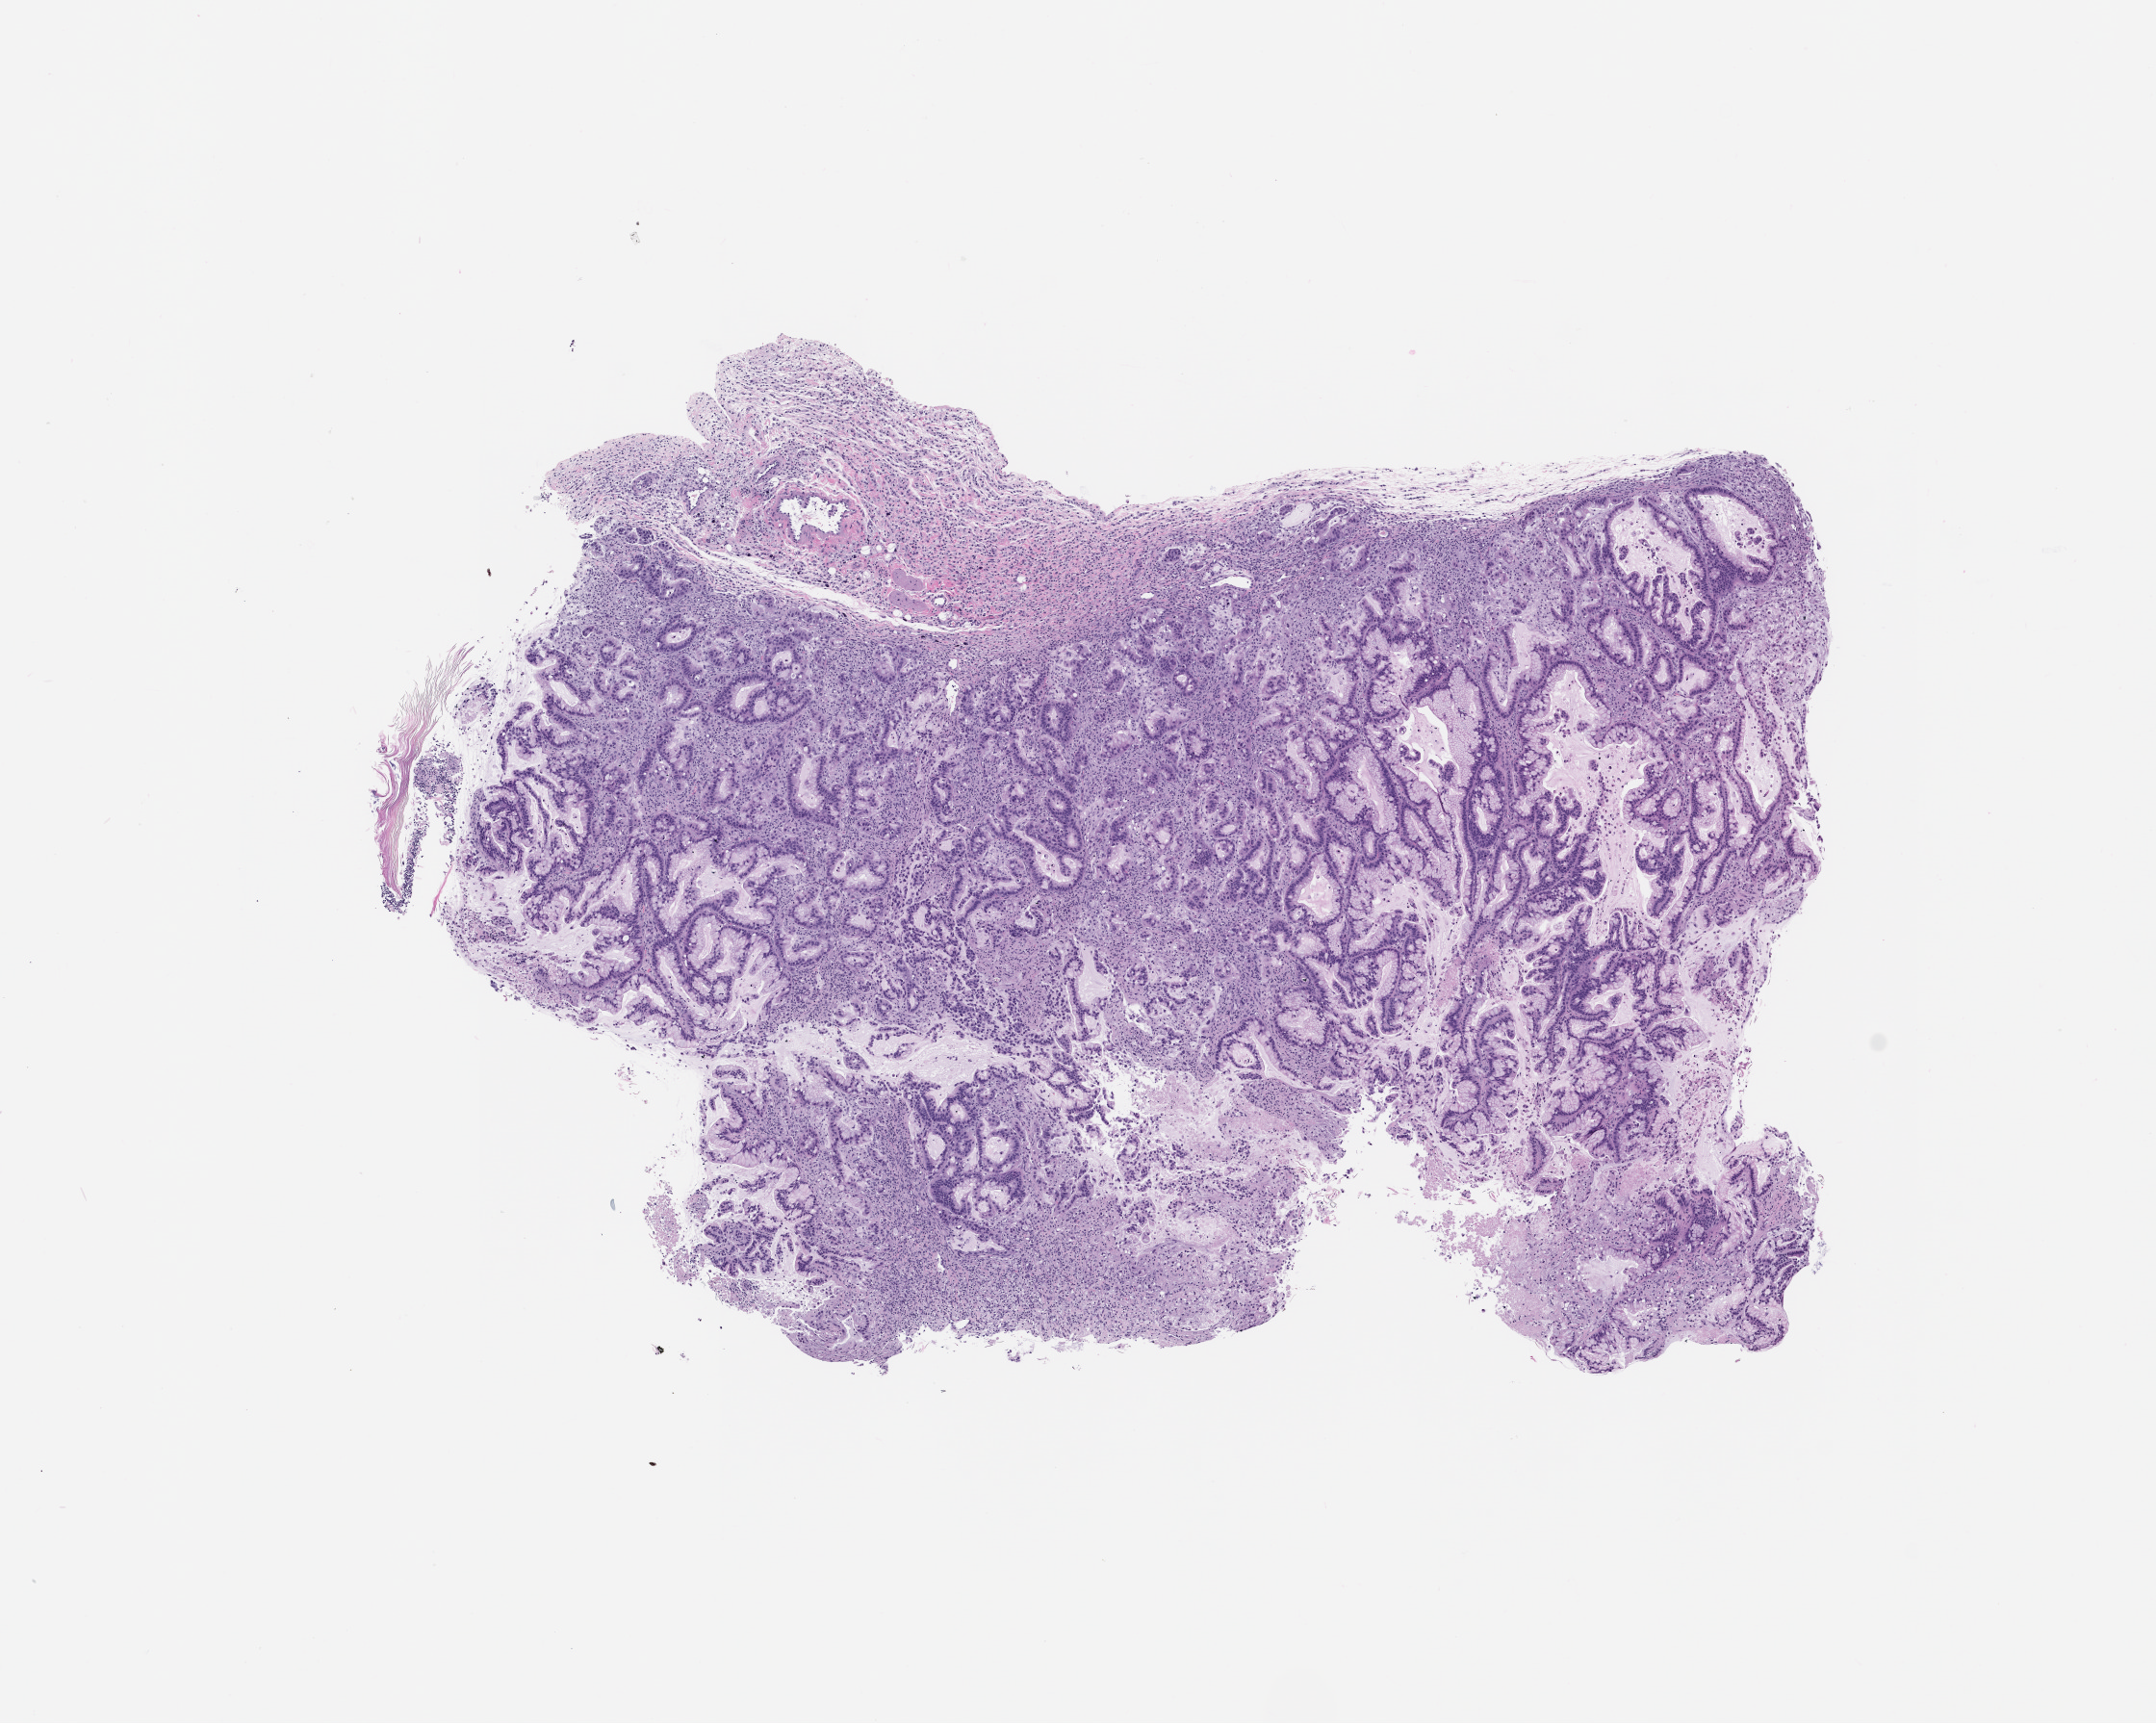
Haematoxylin and eosin whole-slide image of a patient-derived xenograft (PDX) tumor grown in a mouse, passage 0 — a low-resolution overview of the entire scanned area, about 9.0 x 7.2 mm; FFPE section; tumor site category: pancreas.
Originating patient diagnosis: Pancreatic Adenocarcinoma.